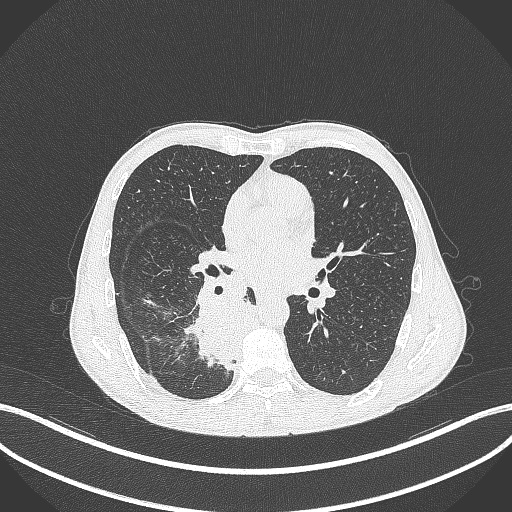
Chest CT, one axial slice; slice 191 of 371 in the series (ordered by position); lung window (W 1500 / L -600 HU); 1 mm slice thickness; 512 × 512 image matrix, field of view 400 × 400 mm. Patient: male, 58 years. From the clinical record (not read from this slice): clinical TNM (as recorded): T3 N1 M1.
Structures marked on this image (bounding box drawn by a radiologist):
- lung tumour (recorded histology: squamous cell carcinoma): bounding box <187,294,255,379> (left, top, right, bottom; pixels)